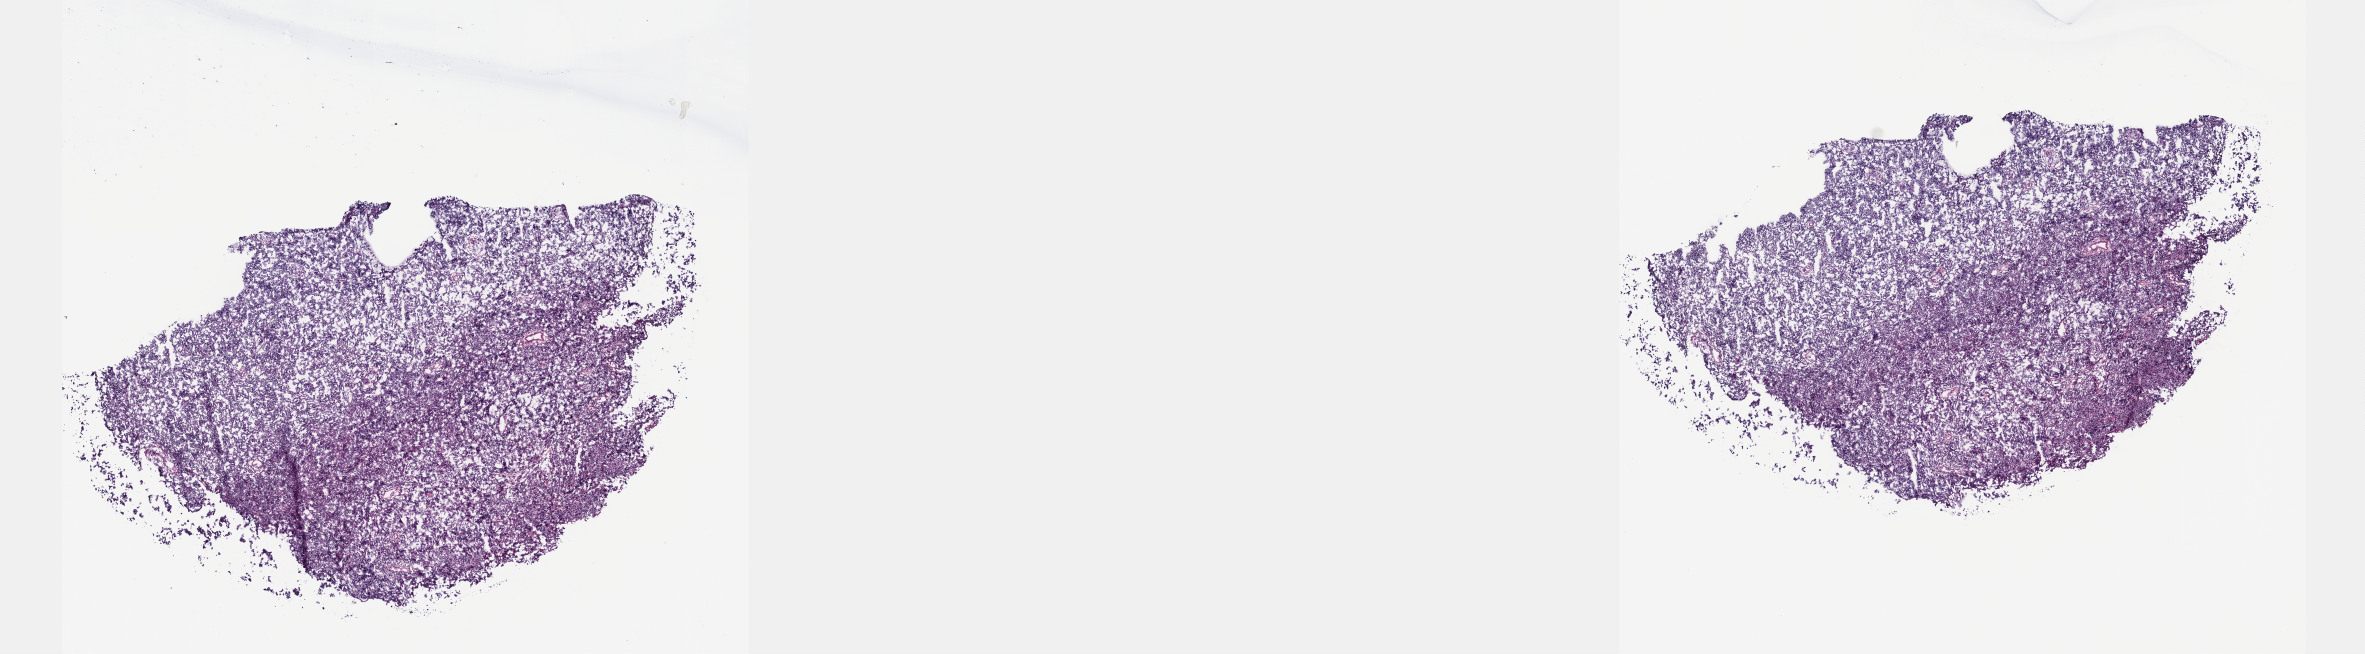
Whole-slide histology image, Hematoxylin and eosin (H&E) stained, a low-resolution overview of the entire scanned area, about 19.1 x 5.3 mm (slide scanned at 40x); frozen section from the top of the tissue portion; testis, primary tumour sample. Male patient; age at initial diagnosis 34 years. Composition of this section per pathologist review: tumour cells 100%, tumour nuclei 80%, normal cells 0%, stromal cells 0%, necrosis 0%. Infiltration values recorded for this section: lymphocyte infiltration 1%, monocyte infiltration 0%, neutrophil infiltration 0%.
AJCC pathologic stage: IA (7th edition). Pathologic diagnosis: Seminoma, NOS.